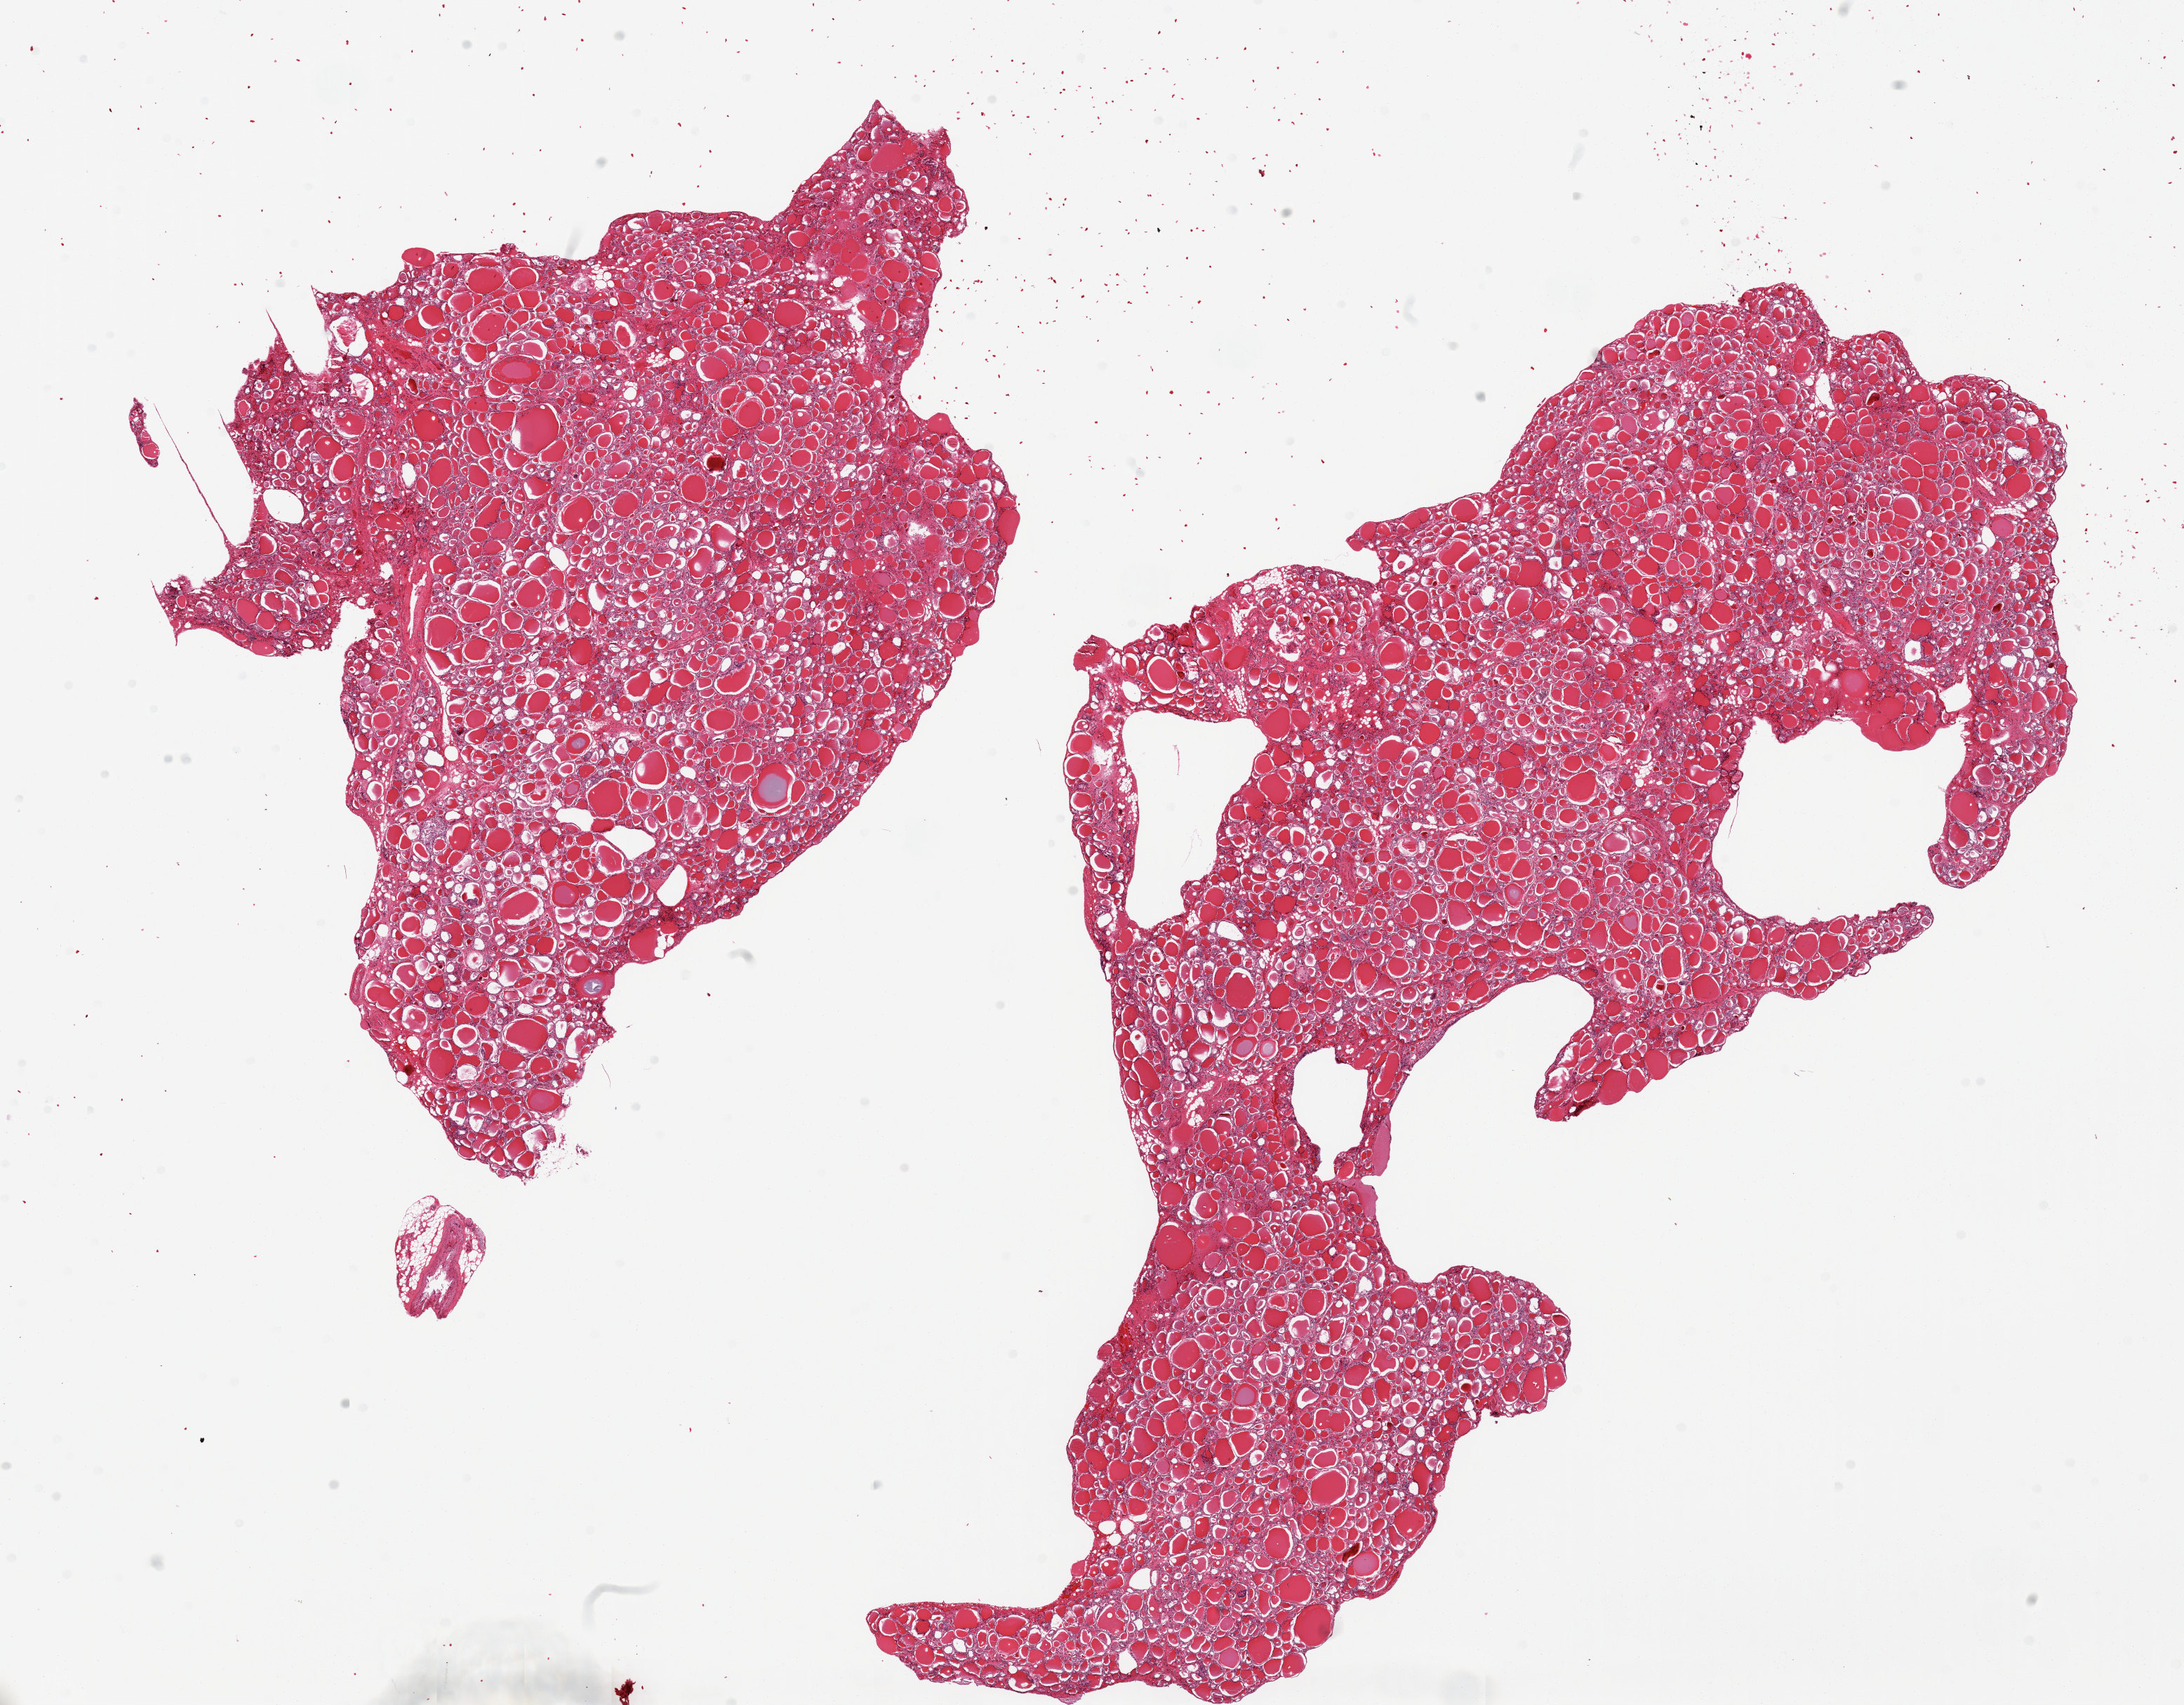
Digitized H&E-stained section, shown as a low-resolution overview of the whole scanned area (about 24.6 x 19.2 mm). PAXgene-fixed paraffin-embedded (PFPE) section. Section of thyroid (target tissue). Donor tissue sample.
- pathologist's review note for this sample: 2 pieces, no abnormalities noted